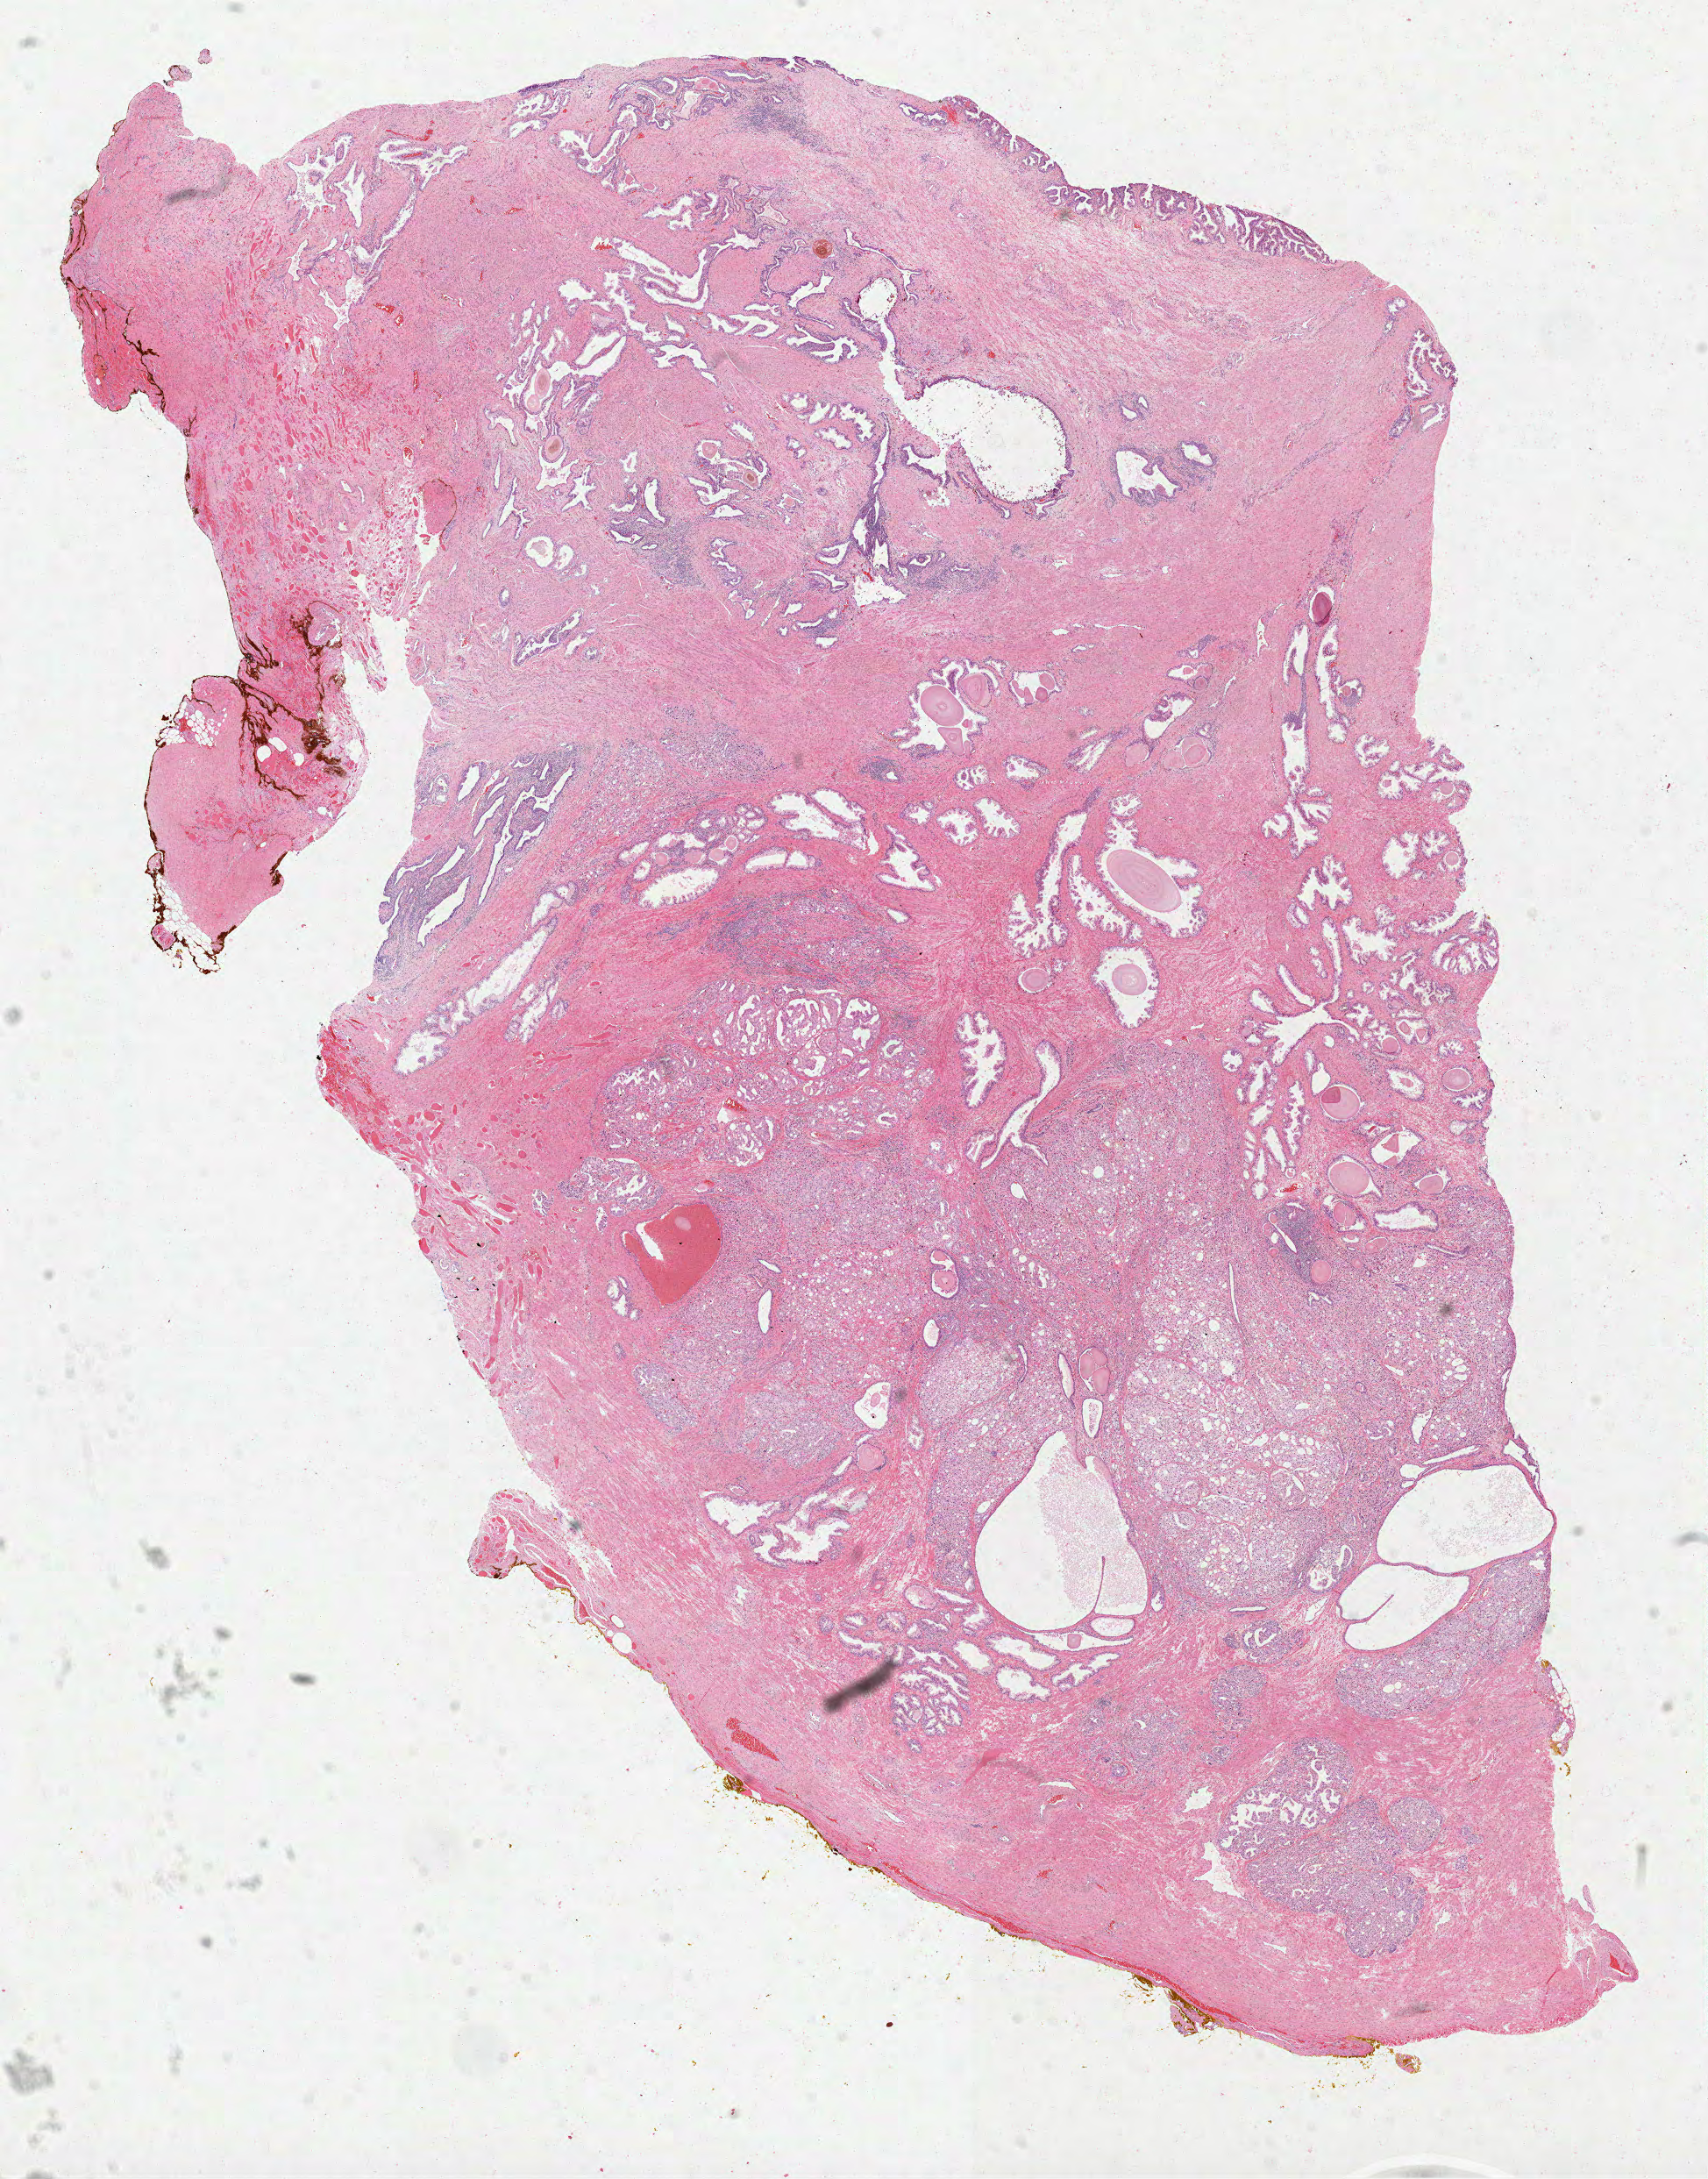
Digitized H&E tissue section (whole slide), shown as a low-resolution overview of the whole scanned area (about 15.7 x 20.0 mm, acquisition: 40x scan); formalin-fixed paraffin-embedded (FFPE) diagnostic section; primary tumour sample from the prostate. Male, age 52 years at initial diagnosis. Gleason score: 8 (4+4).
• lymph nodes positive (case pathology): 1 of 9 examined
• histologic diagnosis: Acinar cell carcinoma (prostate gland)
• laterality: bilateral